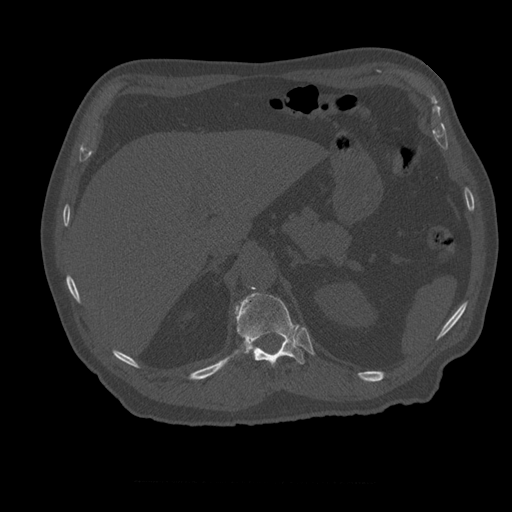
CT including the spine, one axial slice; 120 kVp; bone window (W 1800 / L 400 HU); 1.25 mm slice thickness; 512 × 512 image matrix, field of view 407 × 407 mm. Patient age 73 years. Case-level facts recorded for this patient, not image findings: primary cancer: prostate; vertebrae with lytic lesions (as recorded): L2.
Structures marked on this image (semi-automatically segmented with operator editing):
- T12 vertebra: box from (x=235, y=293) to (x=305, y=367) px